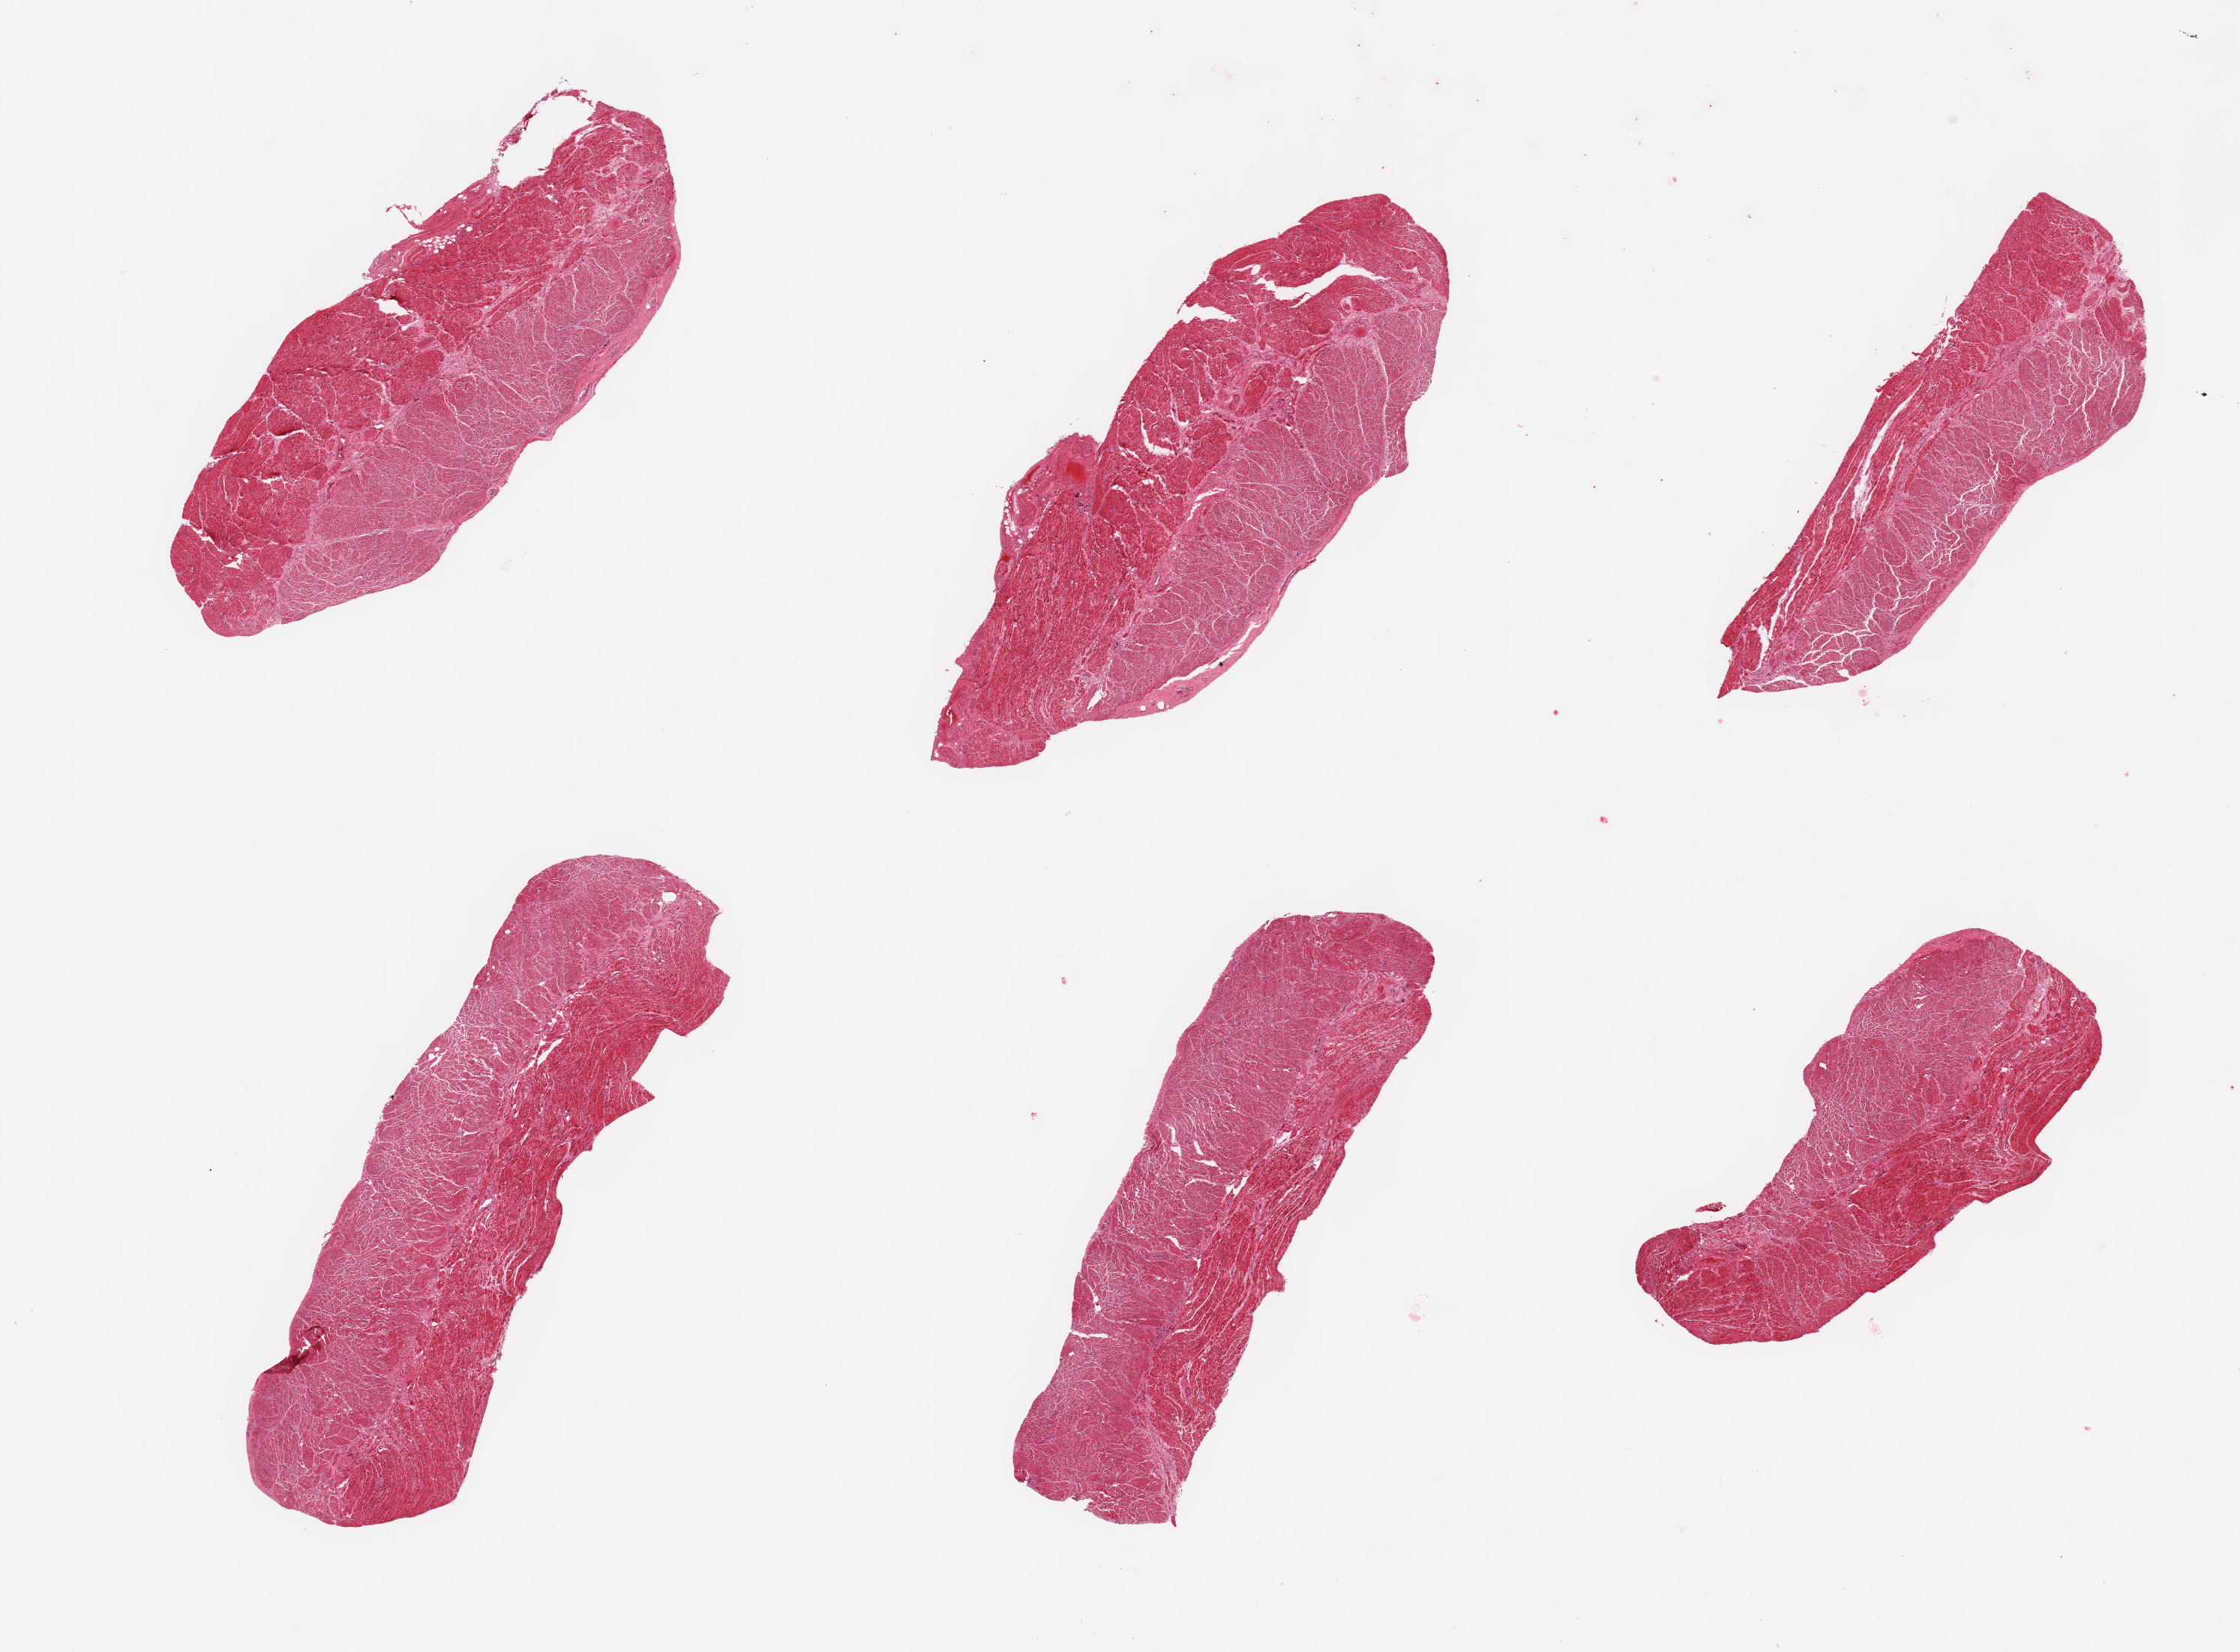
Whole-slide image, H&E stain, brightfield, a low-resolution overview of the entire scanned area, about 23.6 x 17.4 mm (slide scanned at 20x), PAXgene-fixed, paraffin-embedded tissue, sampled site (target tissue): esophageal muscle, donor tissue sample. Donor sex: male.
Review note (as recorded): 6 pieces; target muscularis.